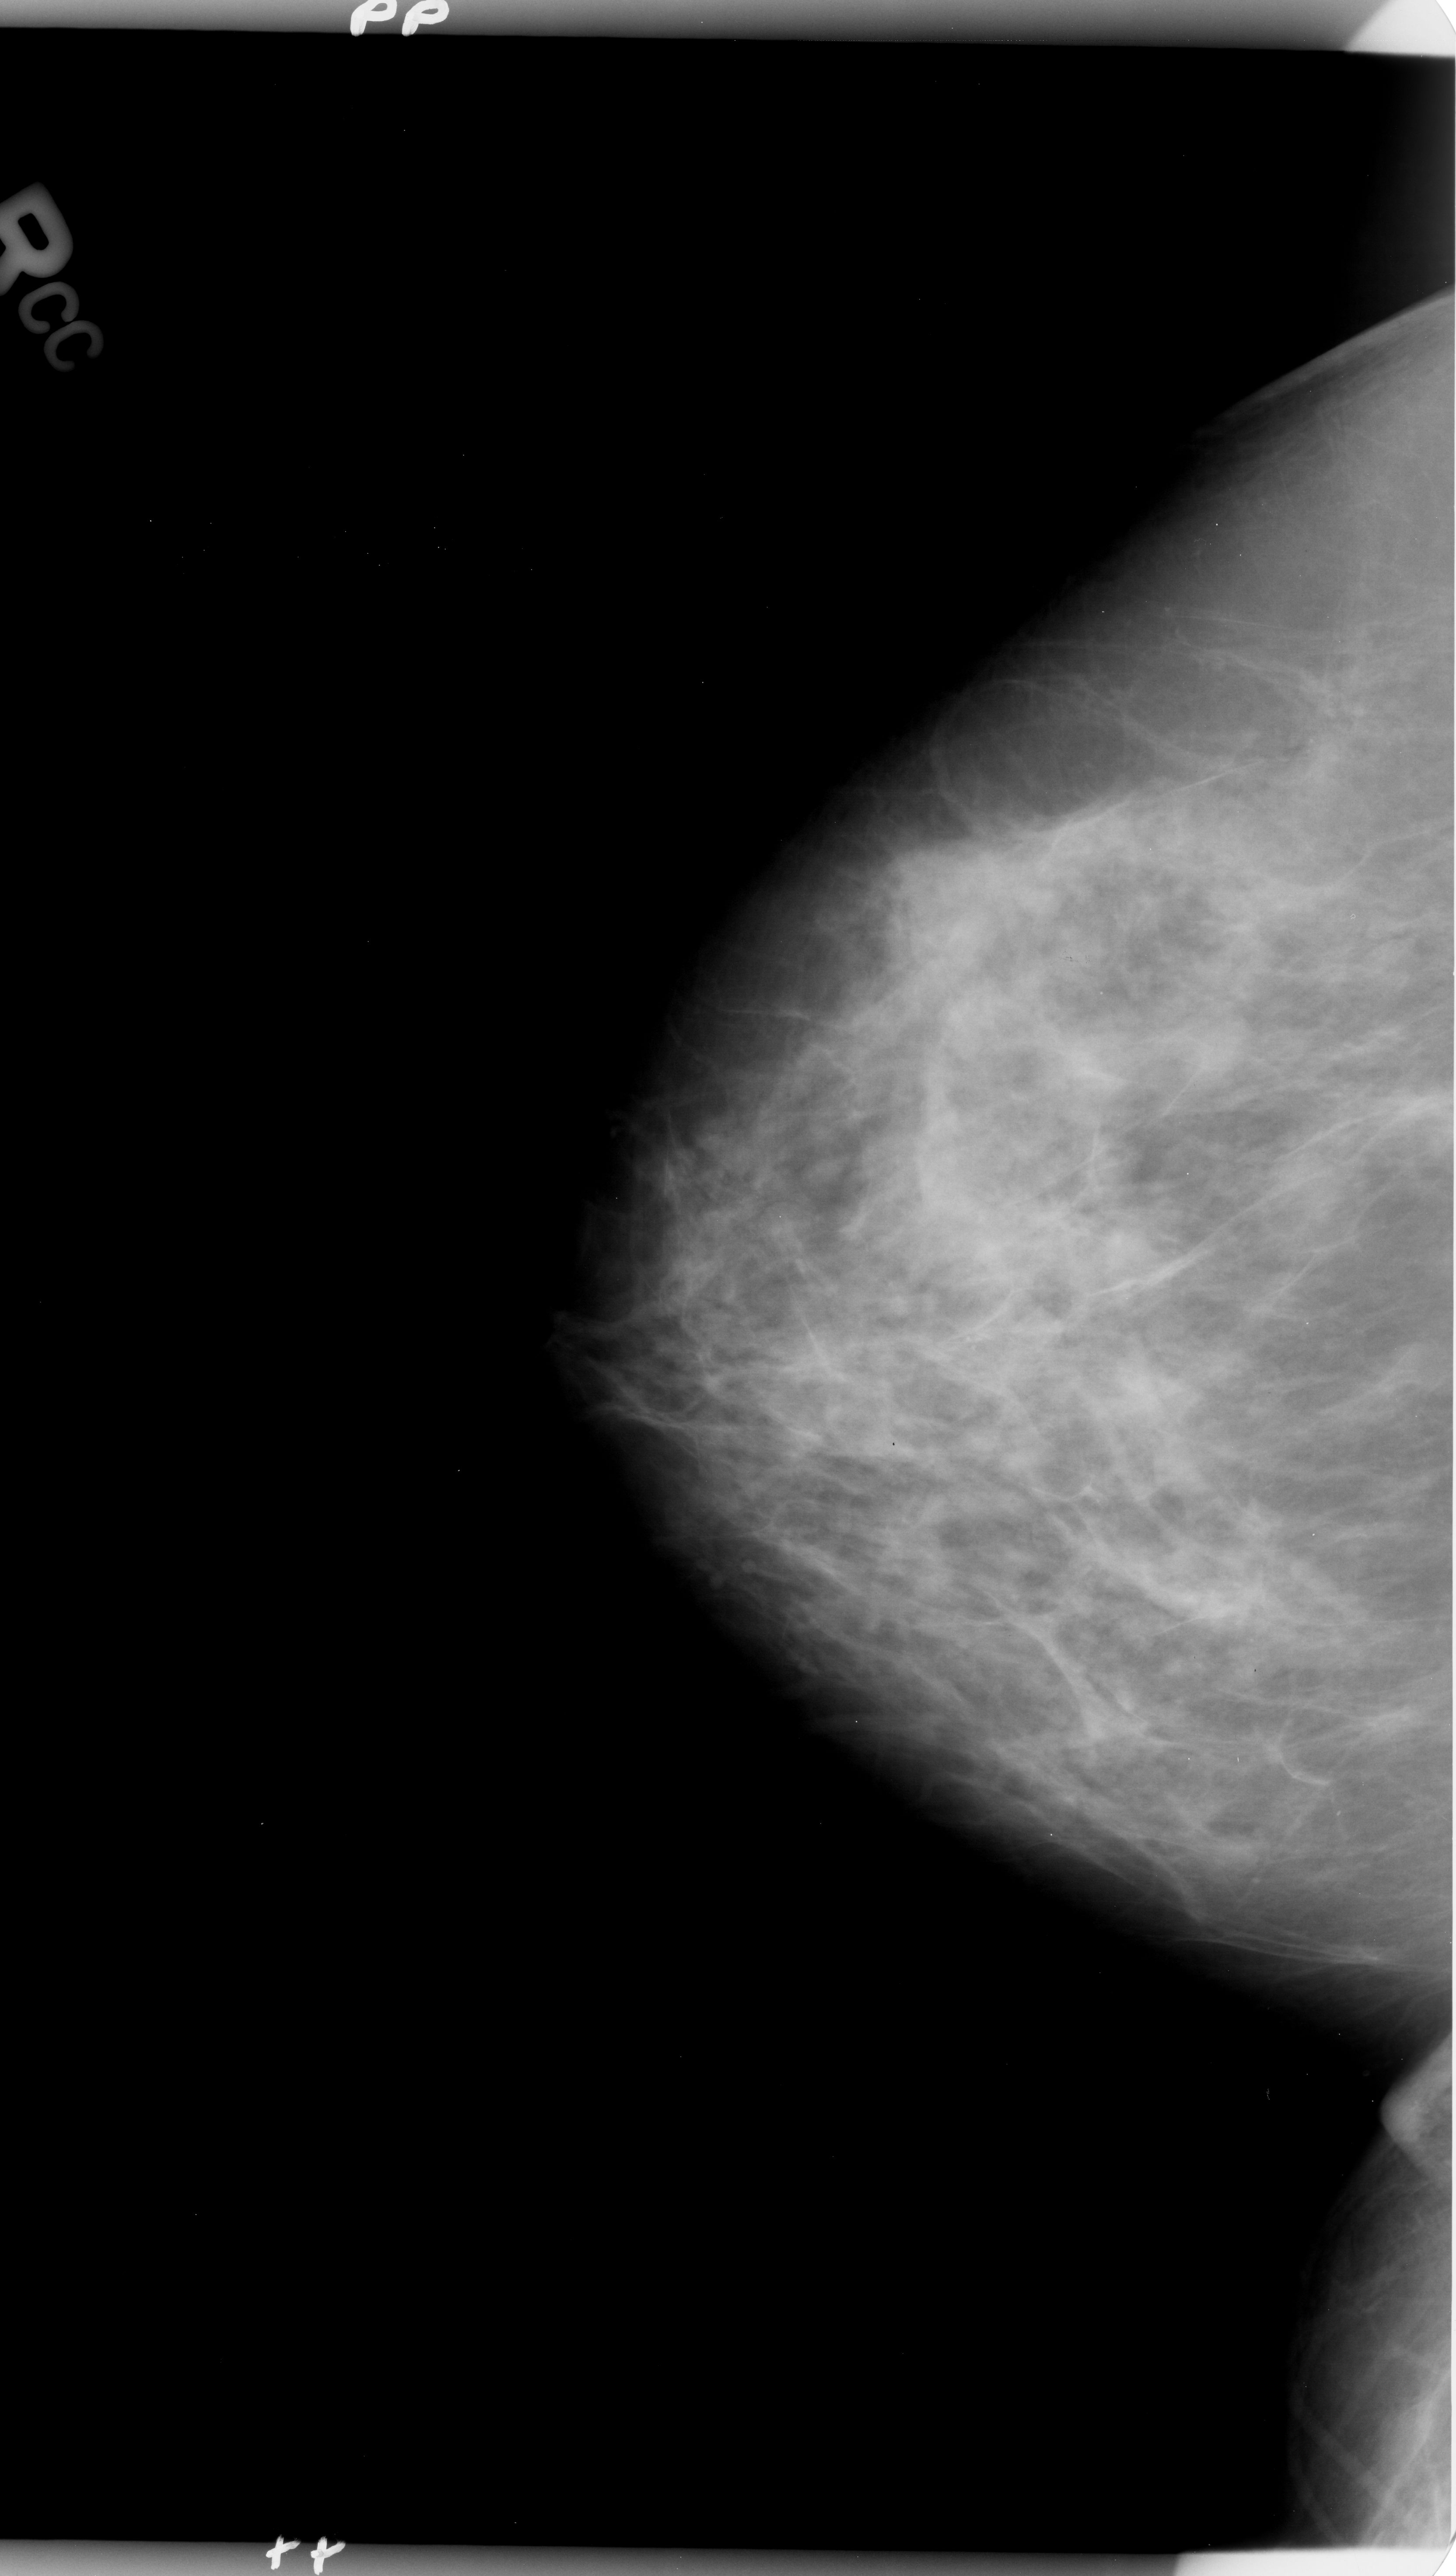
Scanned film-screen mammogram; right breast; craniocaudal (CC) view; breast composition: heterogeneously dense (BI-RADS density category 3 of 4).
Marked findings (only marked abnormalities are described; nothing is implied about the rest of the image): Finding 1 of 2: calcifications, morphology amorphous / pleomorphic, distribution clustered; BI-RADS assessment category 4; pathology result (as recorded, not read from the image): benign. Finding 2 of 2: calcifications, morphology amorphous / pleomorphic, distribution clustered; BI-RADS assessment category 4; pathology (as recorded): benign.